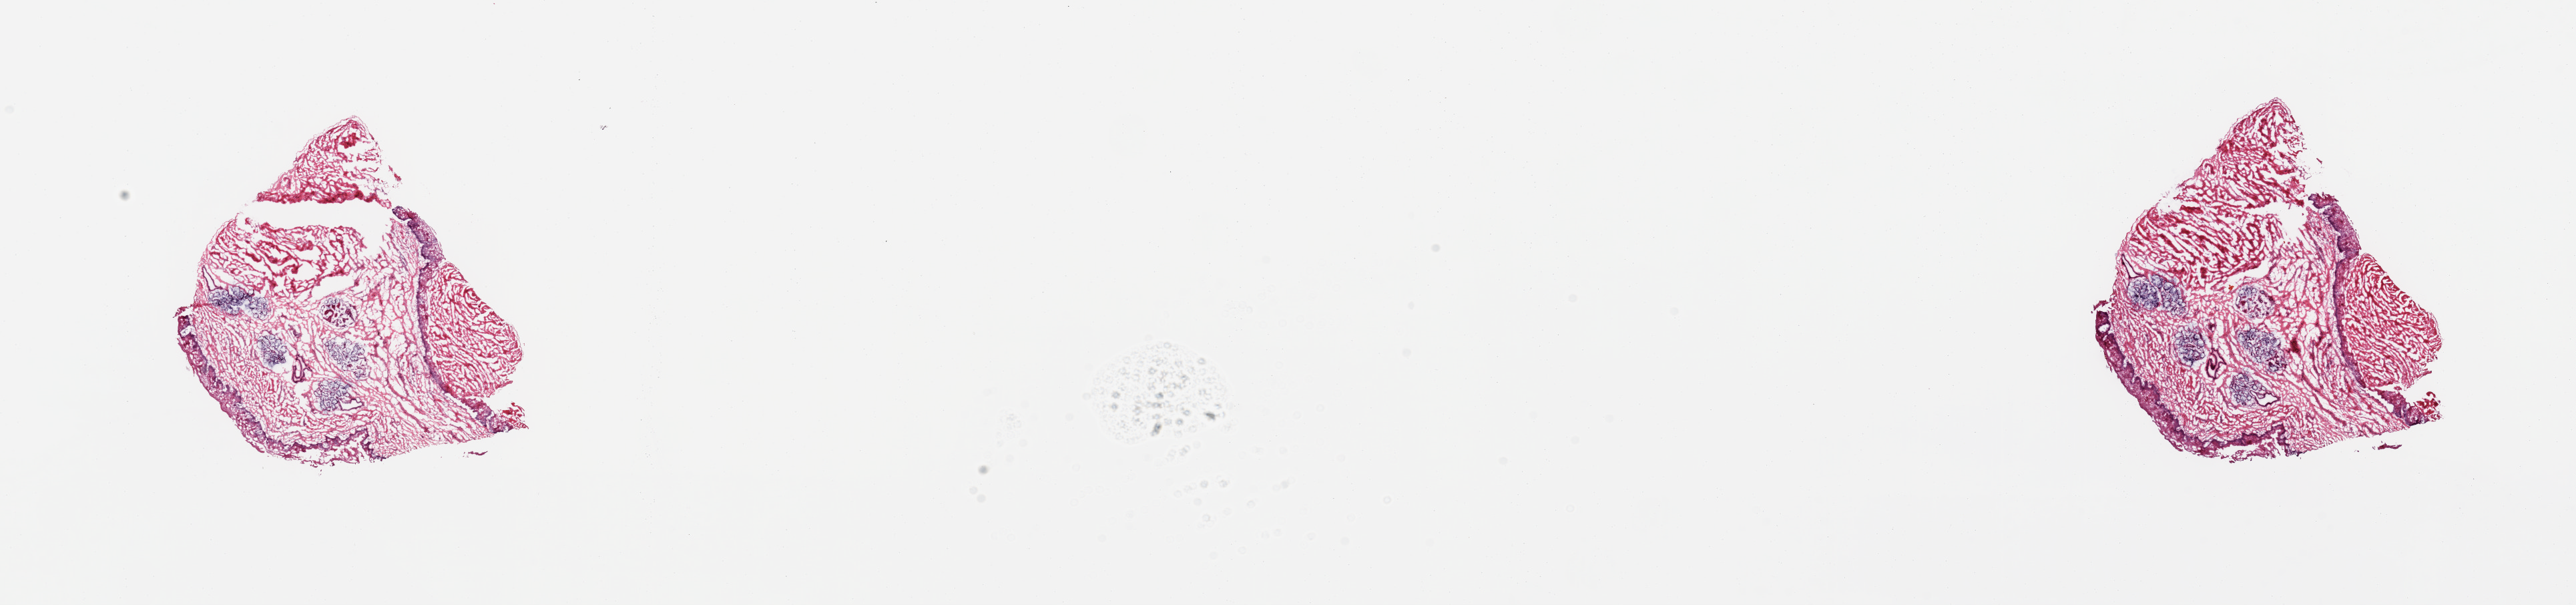
Digitized hematoxylin and eosin (H&E)-stained section, shown as a low-resolution overview of the whole scanned area (about 30.5 x 7.2 mm, slide scanned at 20x). Female donor.
Specimen: frozen section (dry ice); target tissue: esophageal mucous membrane; donor tissue sample.